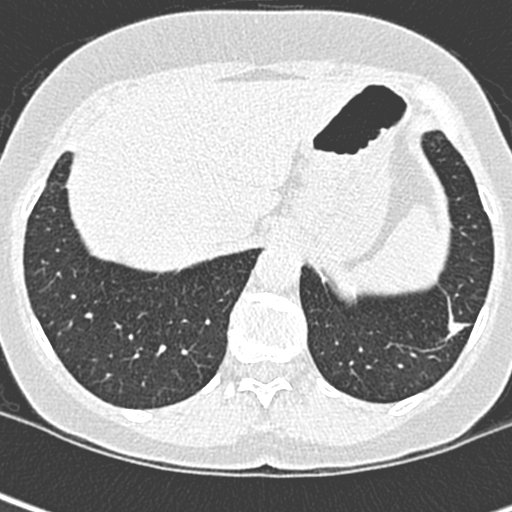
Low-dose screening chest CT, one axial slice; slice 55 of 252 in the series (ordered by position); lung window (W 1500 / L -600 HU); 512 × 512 image matrix, field of view 271 × 271 mm.
Annotated regions visible in this slice (outlined manually by an expert reader):
- lesion 1 (tumor, lower lobe of left lung): bounding box (x1, y1, x2, y2) in pixels: (447, 315, 461, 336)